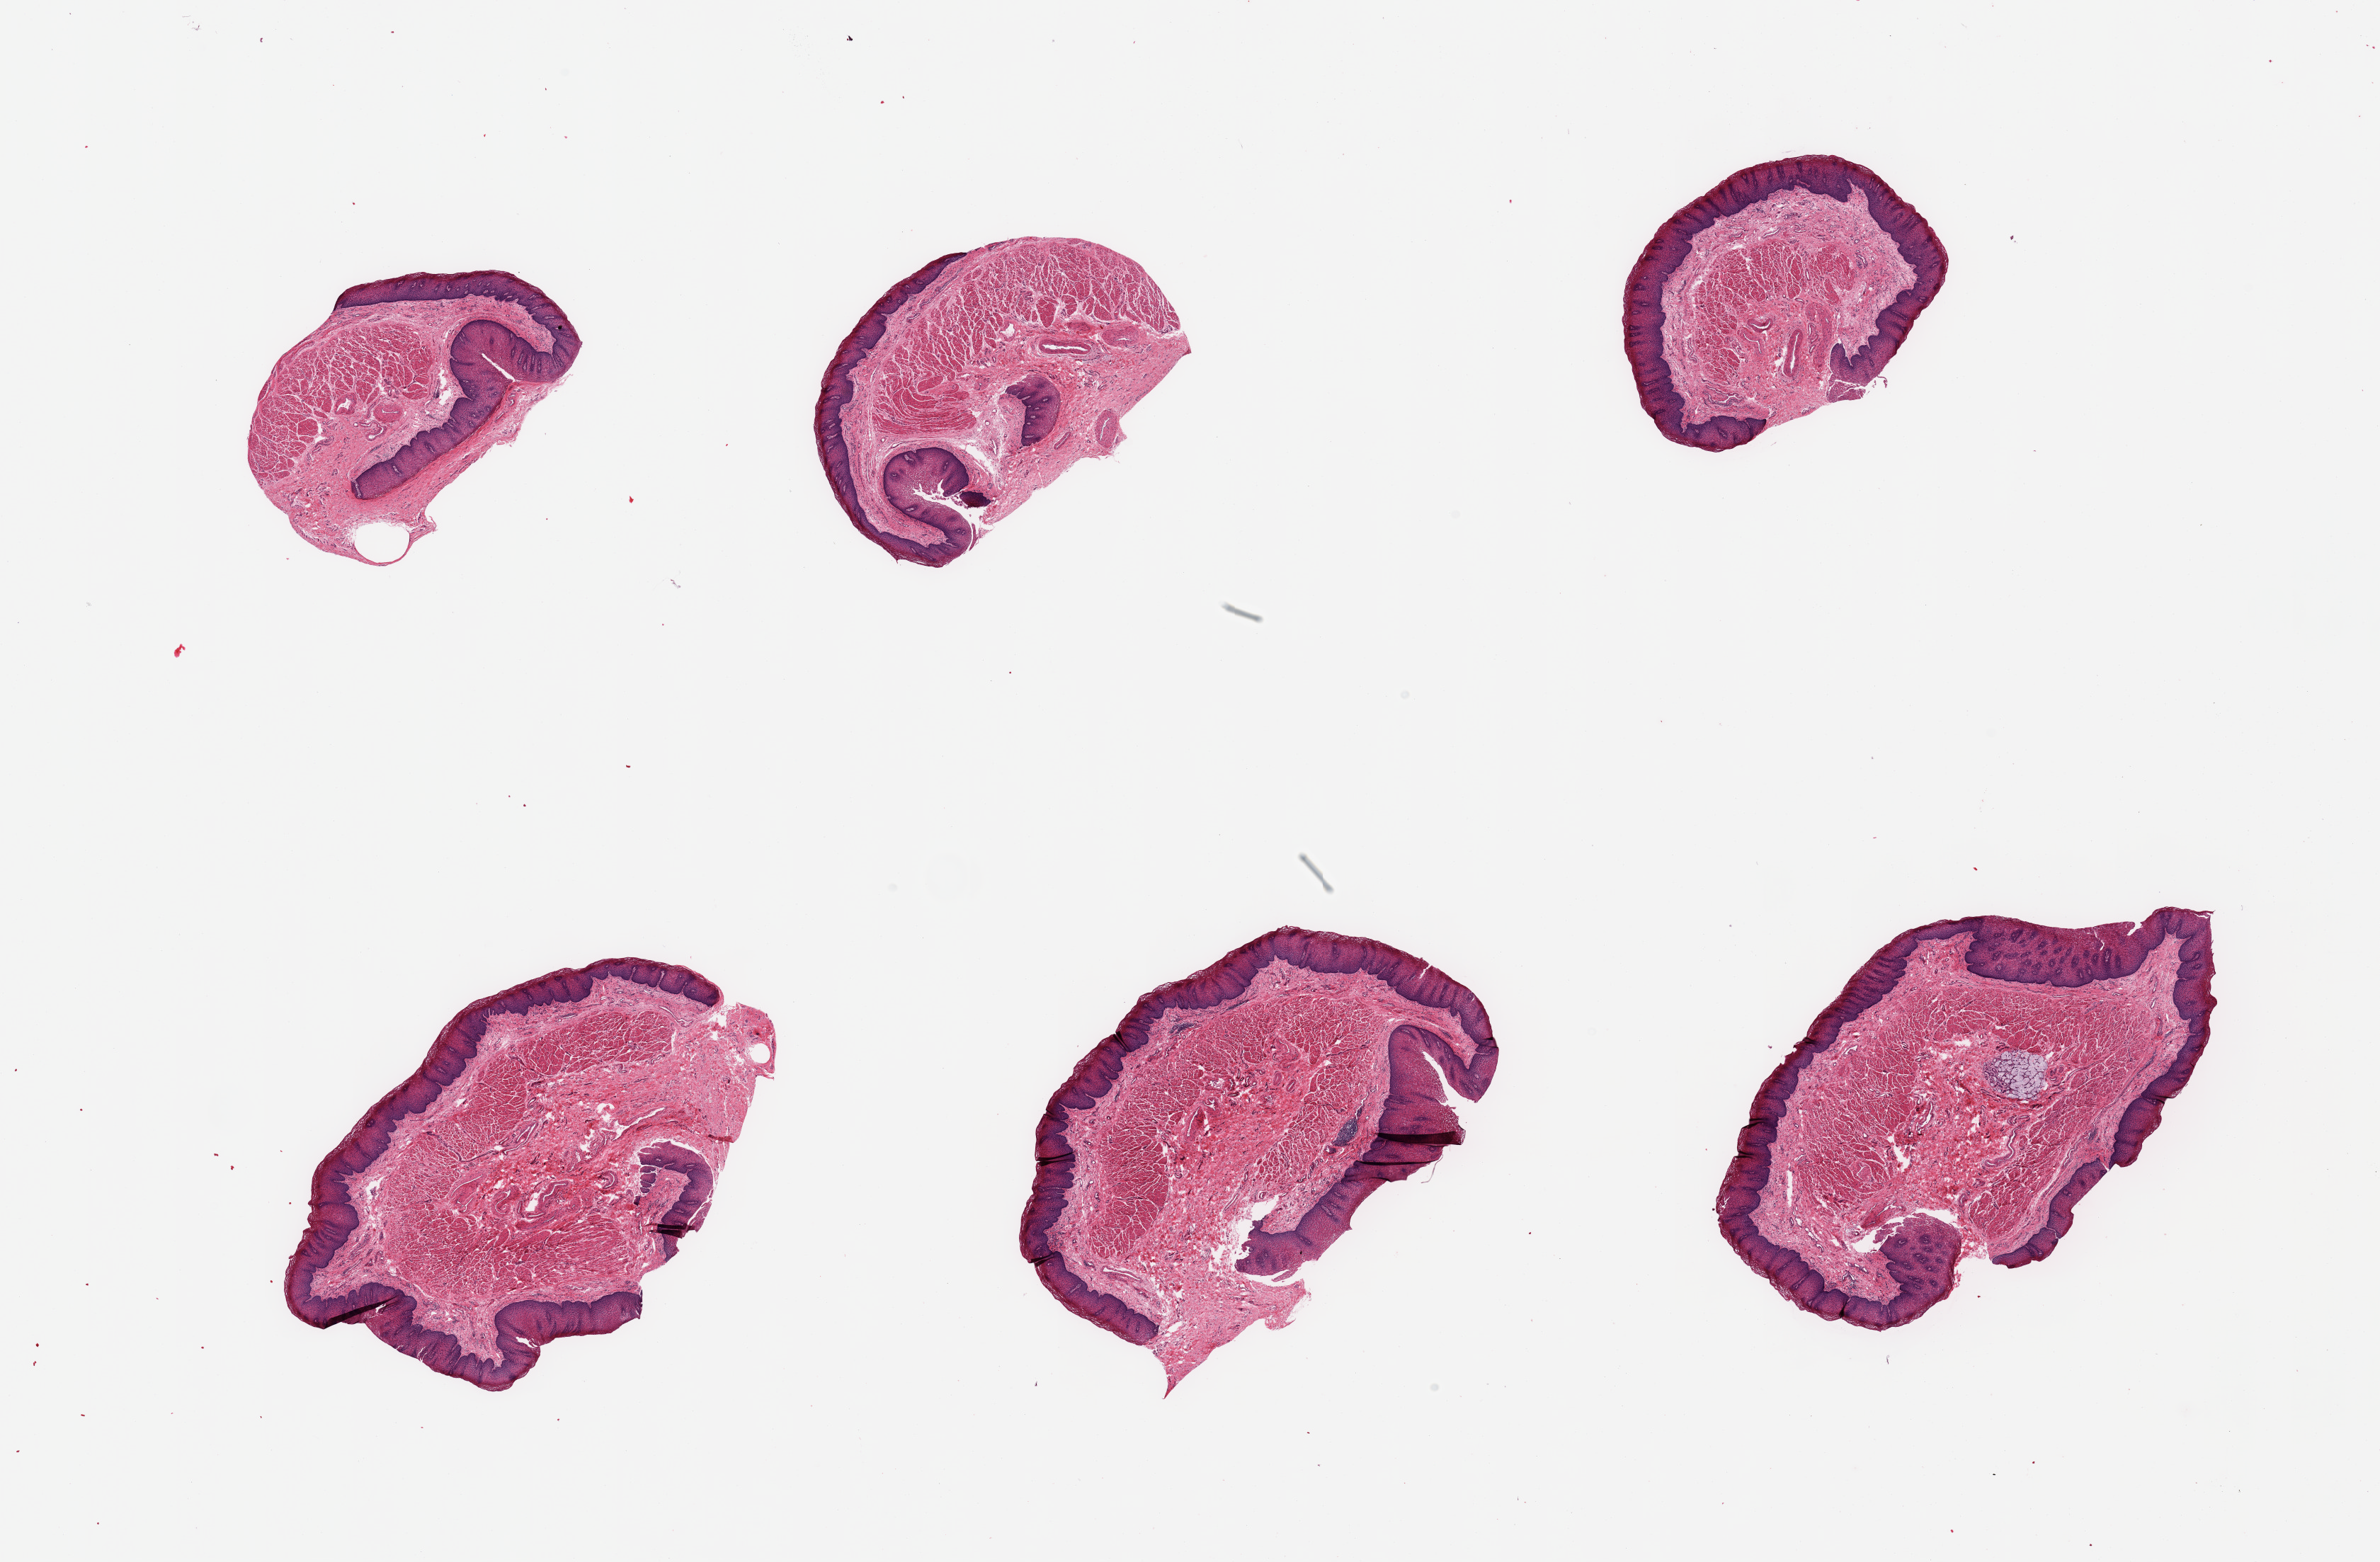
Digitized haematoxylin and eosin-stained section — shown as a low-resolution overview of the whole scanned area (about 26.6 x 17.4 mm); PAXgene-fixed, paraffin-embedded tissue; section of esophageal mucous membrane (target tissue); donor tissue sample. Donor: male.
- pathologist's review note for this sample: 6 pieces; squamous mucosa up to ~0.35mm, ~25% thickness; Rare mucus glands present